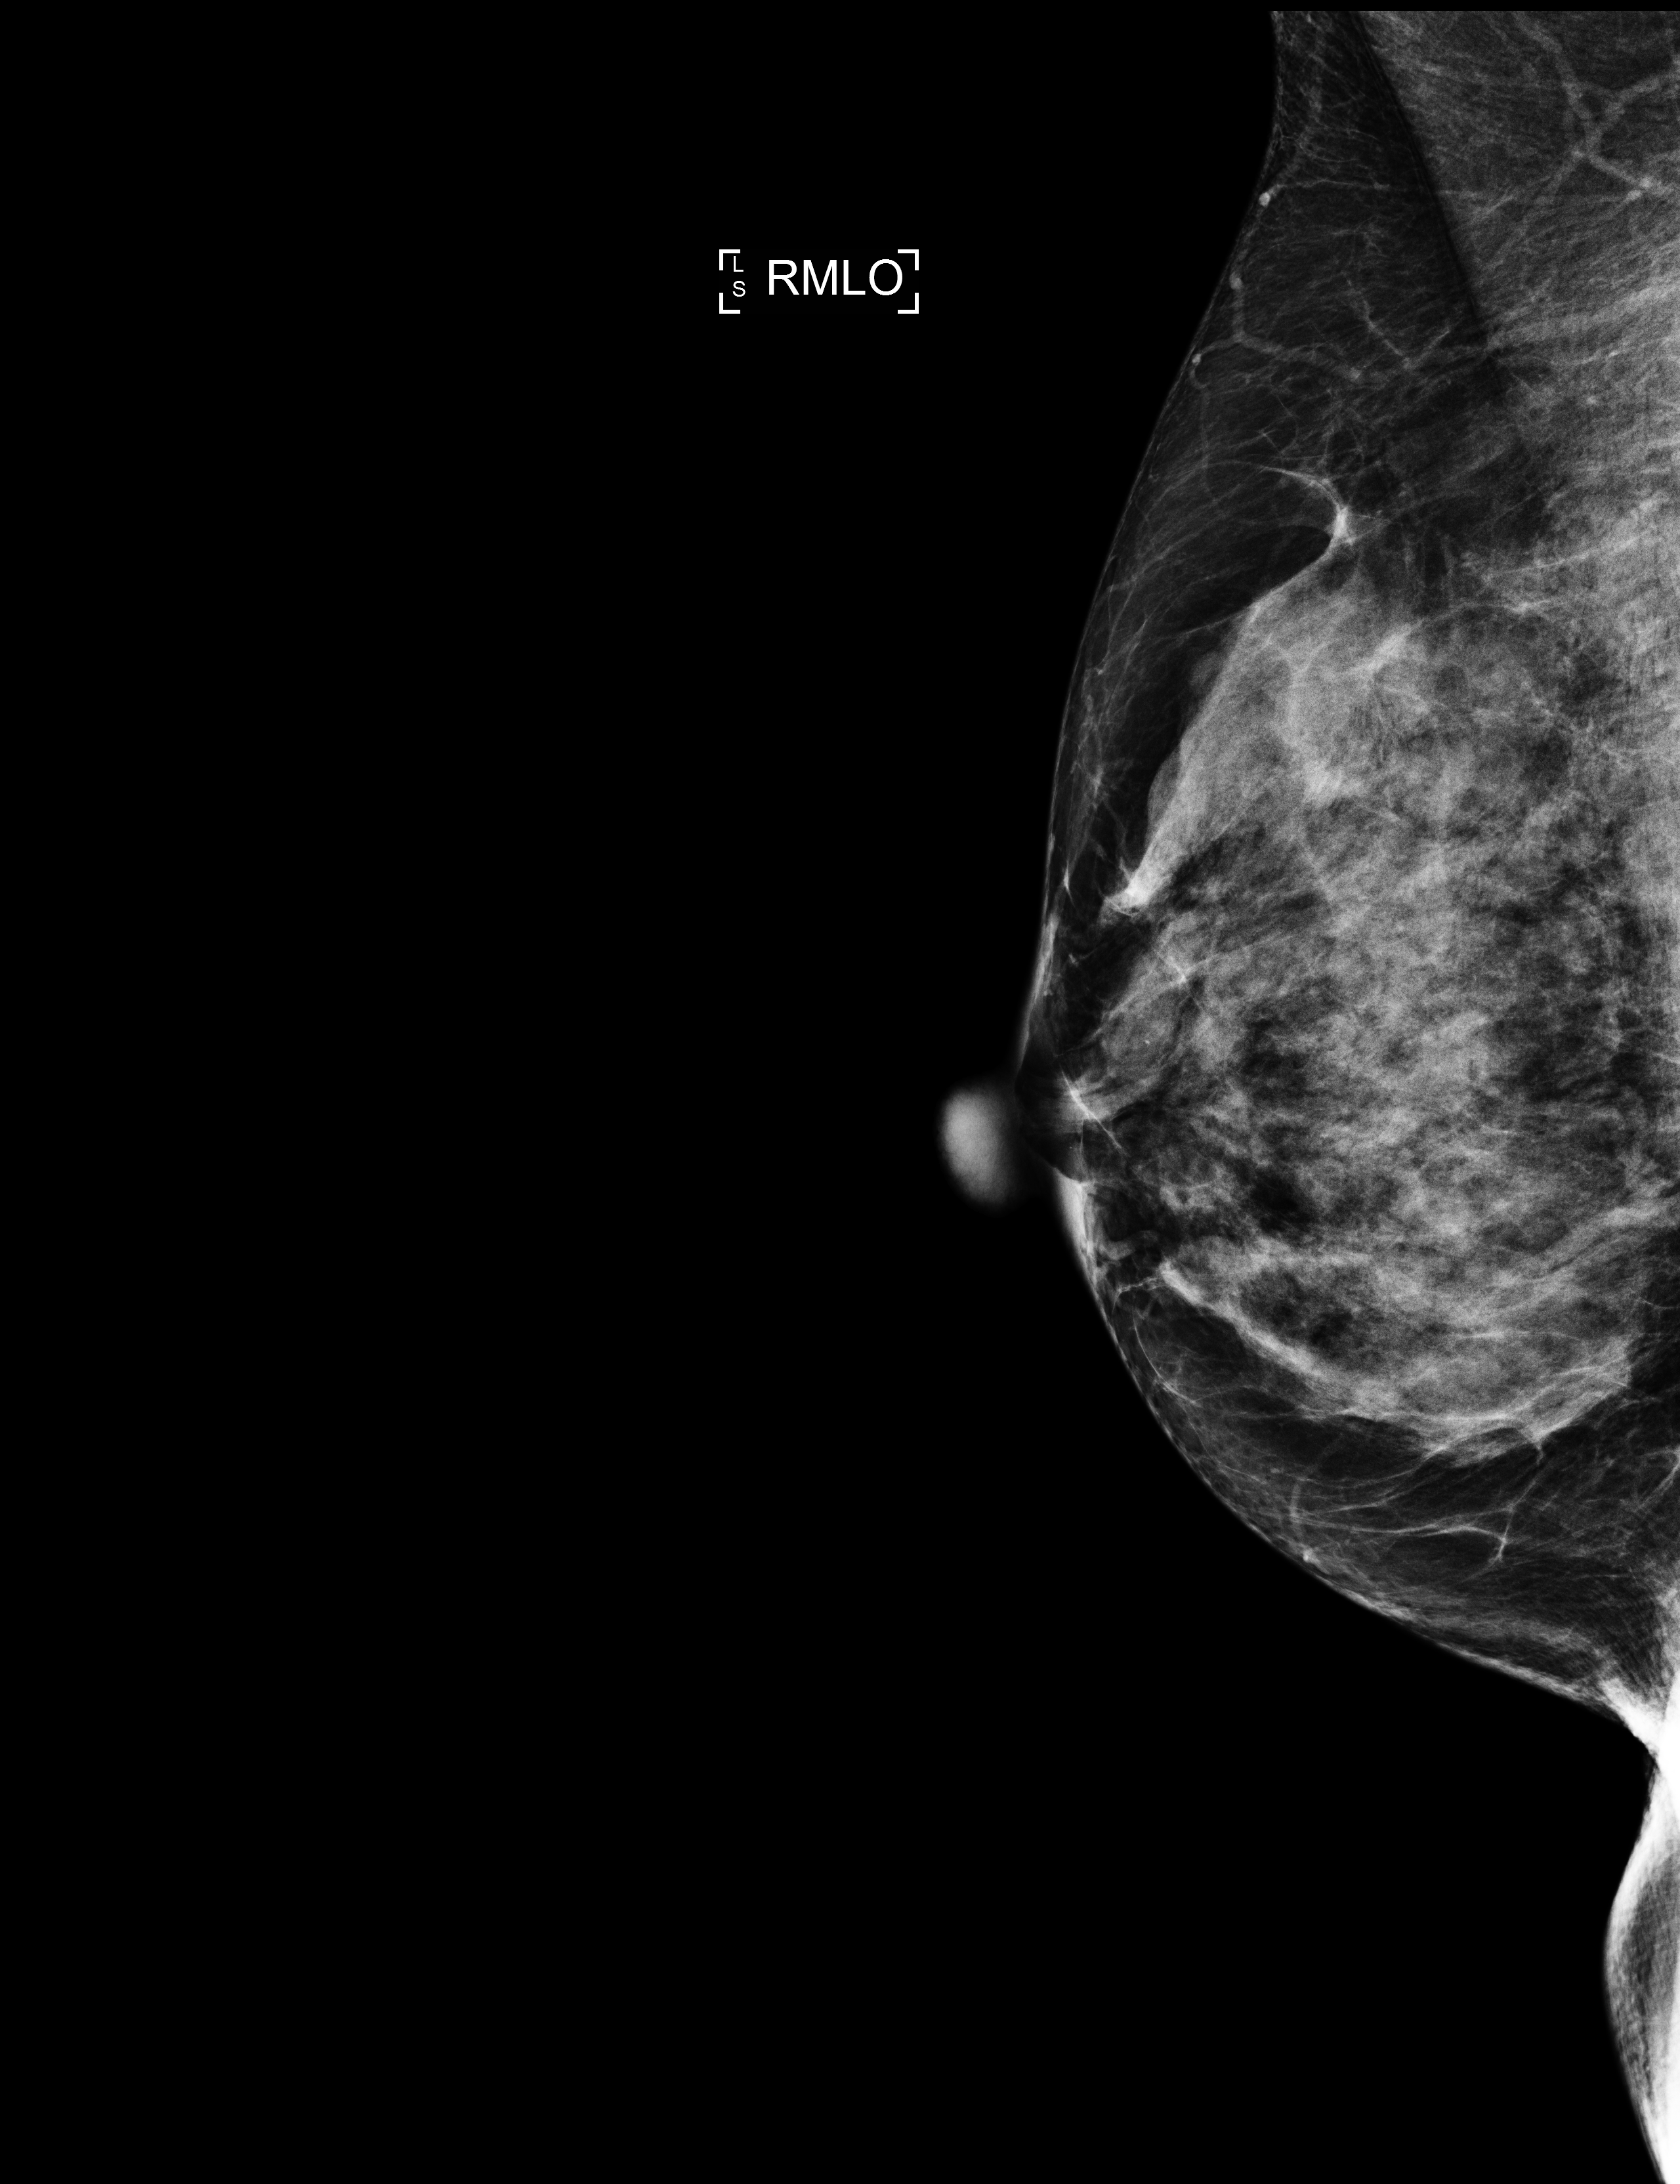
Screening examination; compressed breast thickness 46 mm; system: Selenia Dimensions. Female patient, age 68 years.
Image type: full-field digital mammogram. Breast: right. Projection: medio-lateral oblique projection.